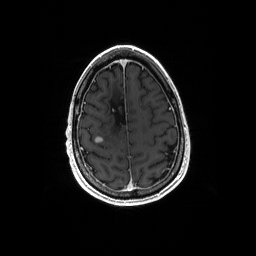
Brain MRI from a brain-tumour surgery series, one axial slice; position 46 of 192 along the scan axis; T1-weighted post-contrast; 1 mm slice thickness; 256 × 256 image matrix, field of view 256 × 256 mm. From the clinical record (not read from this slice): histopathology: Astrocytoma; WHO grade: 4; IDH mutation: yes.
Structures marked on this image (manually delineated by an expert):
- tumour: bounding box [x1, y1, x2, y2] px = [95, 137, 102, 144]